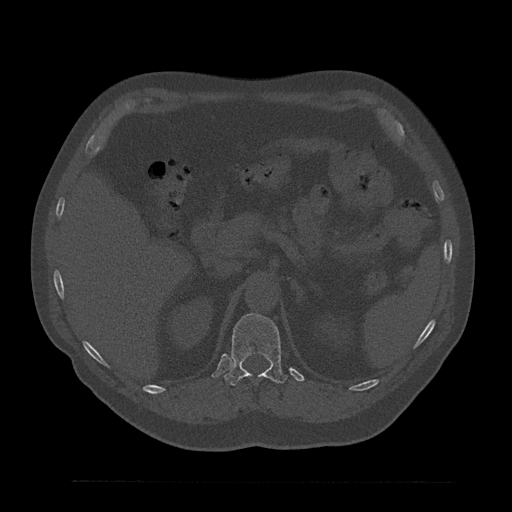
CT including the spine, one axial slice; position 235 of 797 along the scan axis; bone window (W 1800 / L 400 HU); 512 × 512 image matrix, field of view 430 × 430 mm. Patient: male, 61 years. Case-level facts recorded for this patient, not image findings: primary cancer: prostate.
Outlined on this slice (semi-automatic segmentation, software-assisted and operator-edited):
- T12 vertebra: box from (x=224, y=313) to (x=287, y=386) px